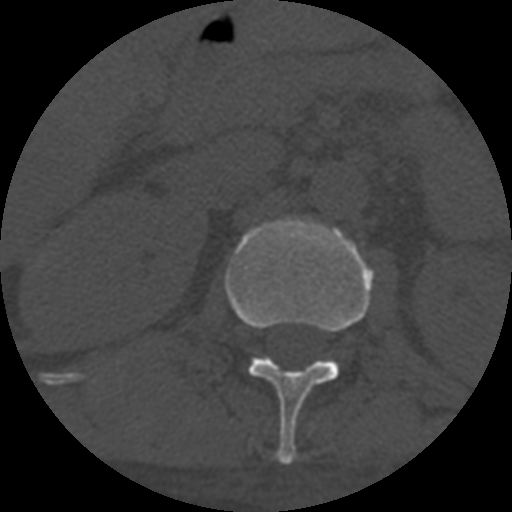
CT including the spine, one axial slice. Position 282 of 708 along the scan axis. One of 3 acquisitions stored at this slice position. Bone window (W 1800 / L 400 HU). 1.25 mm slice thickness. 512 × 512 image matrix, field of view 160 × 160 mm. Patient age 55 years. From the clinical record (not read from this slice): primary cancer: colon.
Annotated regions visible in this slice (semi-automatically segmented with operator editing):
- L1 vertebra: bounding box [x1, y1, x2, y2] px = [224, 216, 374, 465]